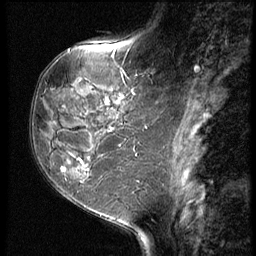
Breast MRI (dynamic contrast-enhanced), one sagittal slice. Position 22 of 62 along the scan axis. 3 images stored at this slice position (order not interpretable as contrast timing). 1.5 T. TE 4.2 ms, TR 9 ms. 2.5 mm slice thickness. 256 × 256 image matrix, field of view 180 × 180 mm. Female patient, age 50 years. Case-level facts recorded for this patient, not image findings: setting: breast cancer imaged before/during neoadjuvant chemotherapy; receptor status: HR-positive, HER2-negative.
Outlined on this slice (semi-automatic segmentation, software-assisted and operator-edited):
- analysis volume of interest (the breast-tissue region the enhancement analysis was run in; not a lesion): bounding box [x1, y1, x2, y2] px = [32, 91, 118, 209]
- tumour enhancement mask (voxels above the 140 % enhancement threshold inside the analysis volume of interest): [62, 158, 84, 171]